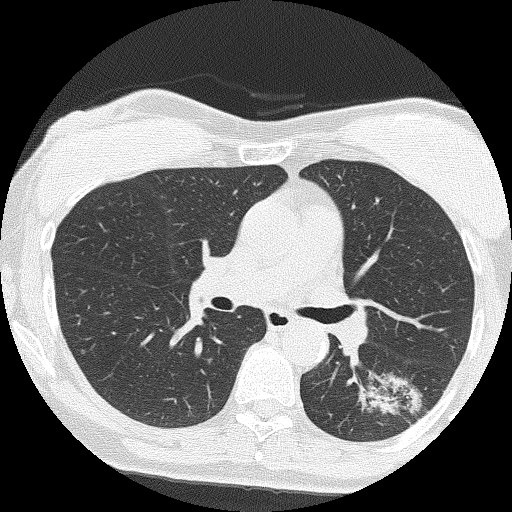
Axial slice from a low-dose chest CT screening exam. Second screening round (one year after baseline). Lung window (W 1500 / L -600 HU). 2 mm slice thickness. Lung (sharp) reconstruction kernel (FC51). Slice 67 of 159 in the series. 512 × 512 image matrix, field of view 303 × 303 mm. Female, age 64 years at enrolment. Former smoker at enrolment.
Lesion marked by an expert reader, box from (x=358, y=370) to (x=438, y=439) px. The screening reader recorded 3 non-calcified nodules or masses ≥4 mm on this exam (right upper lobe, right upper lobe, right middle lobe); which of them this box marks is not recorded. Lung cancer was diagnosed 576 days after this screen: adenocarcinoma, NOS, left lower lobe, moderately differentiated (G2), stage IA (AJCC 6th edition), 17 mm at pathology.